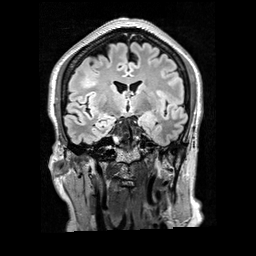
Brain MRI from a brain-tumour surgery series, one coronal slice. Slice 107 of 200 in the series (ordered by position). T2 FLAIR. 1 mm slice thickness. 256 × 256 image matrix, field of view 256 × 256 mm. Case-level facts recorded for this patient, not image findings: histopathology: Glioblastoma; WHO grade: 4; IDH mutation: no; tumour location: Right Frontal.
Annotated regions visible in this slice (expert manual segmentation):
- tumour: box from (x=81, y=72) to (x=99, y=89) px